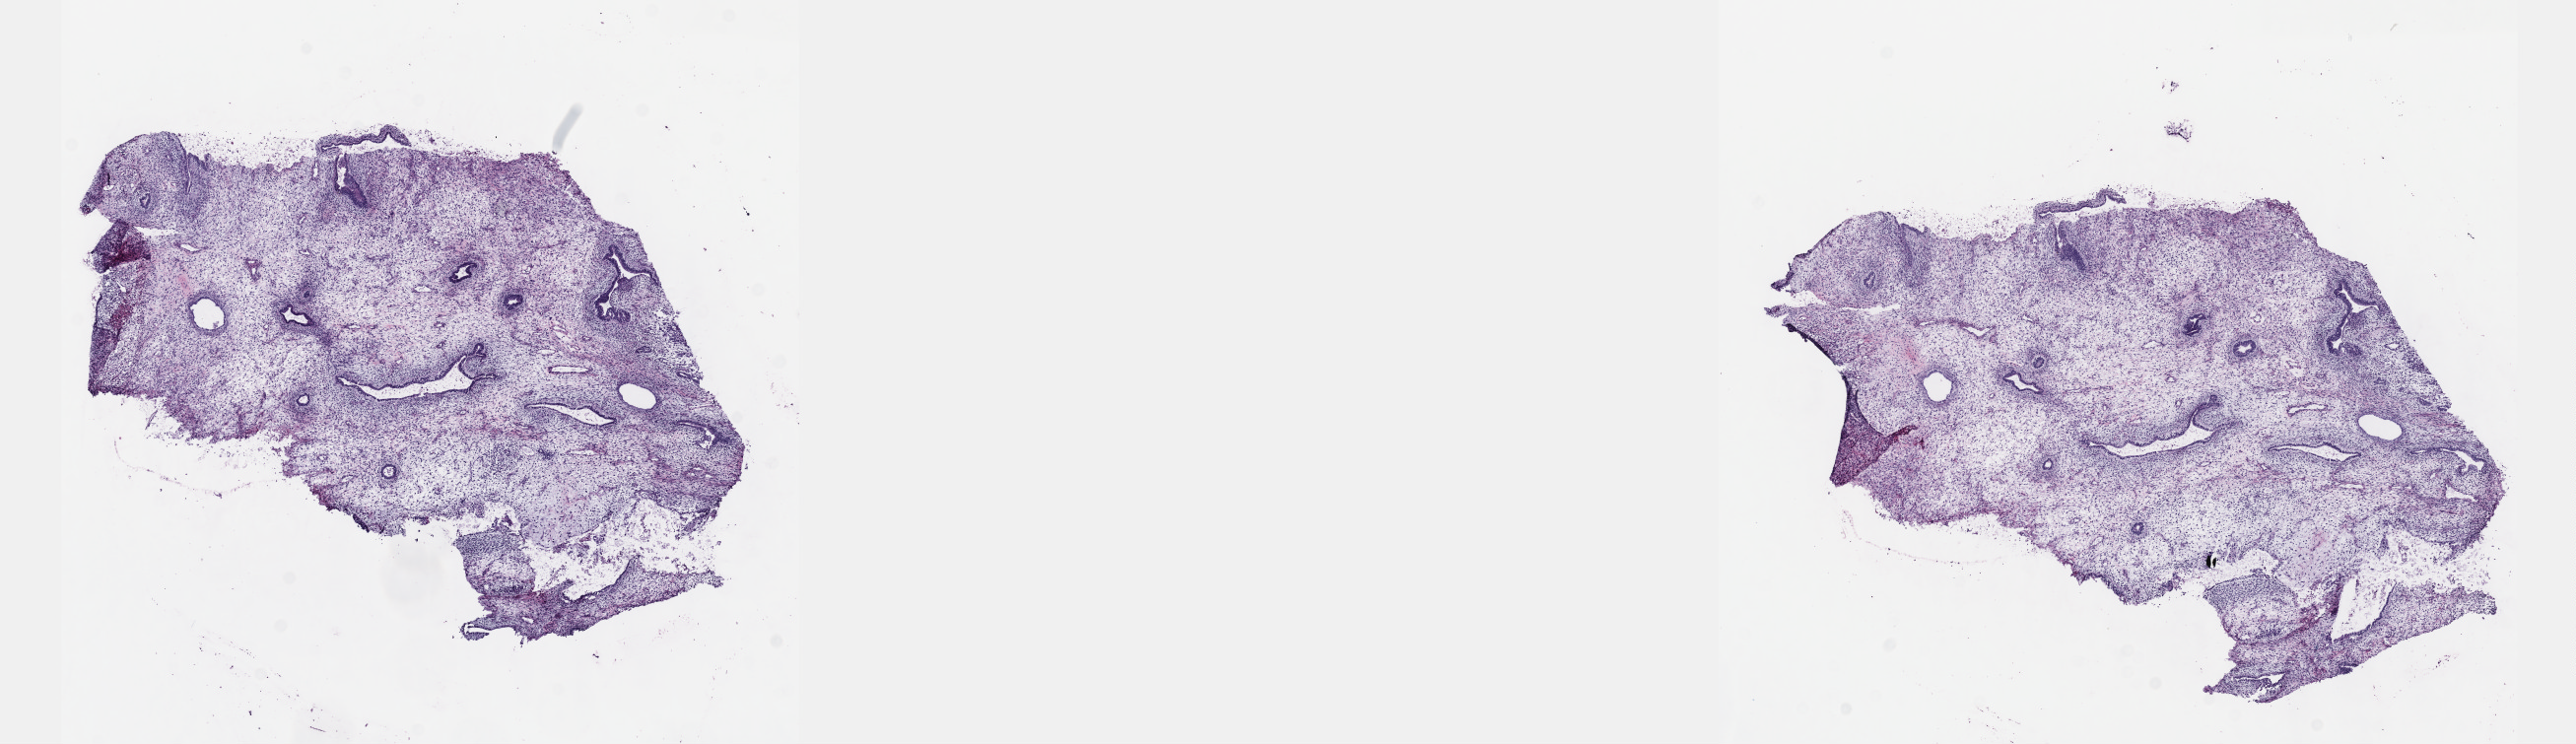
Digitized Hematoxylin and eosin (H&E) stained tissue section (whole slide), whole scanned area (about 21.1 x 6.1 mm, slide scanned at 40x) shown as a low-resolution overview. Male patient. Composition of this section per pathologist review: tumour cells 100%, tumour nuclei 80%, normal cells 0%, stromal cells 0%, necrosis 0%. Infiltration values recorded for this section: lymphocyte infiltration 2%, monocyte infiltration 0%, neutrophil infiltration 0%.
Specimen: frozen section from the top of the tissue portion; sample: primary tumour, testis.